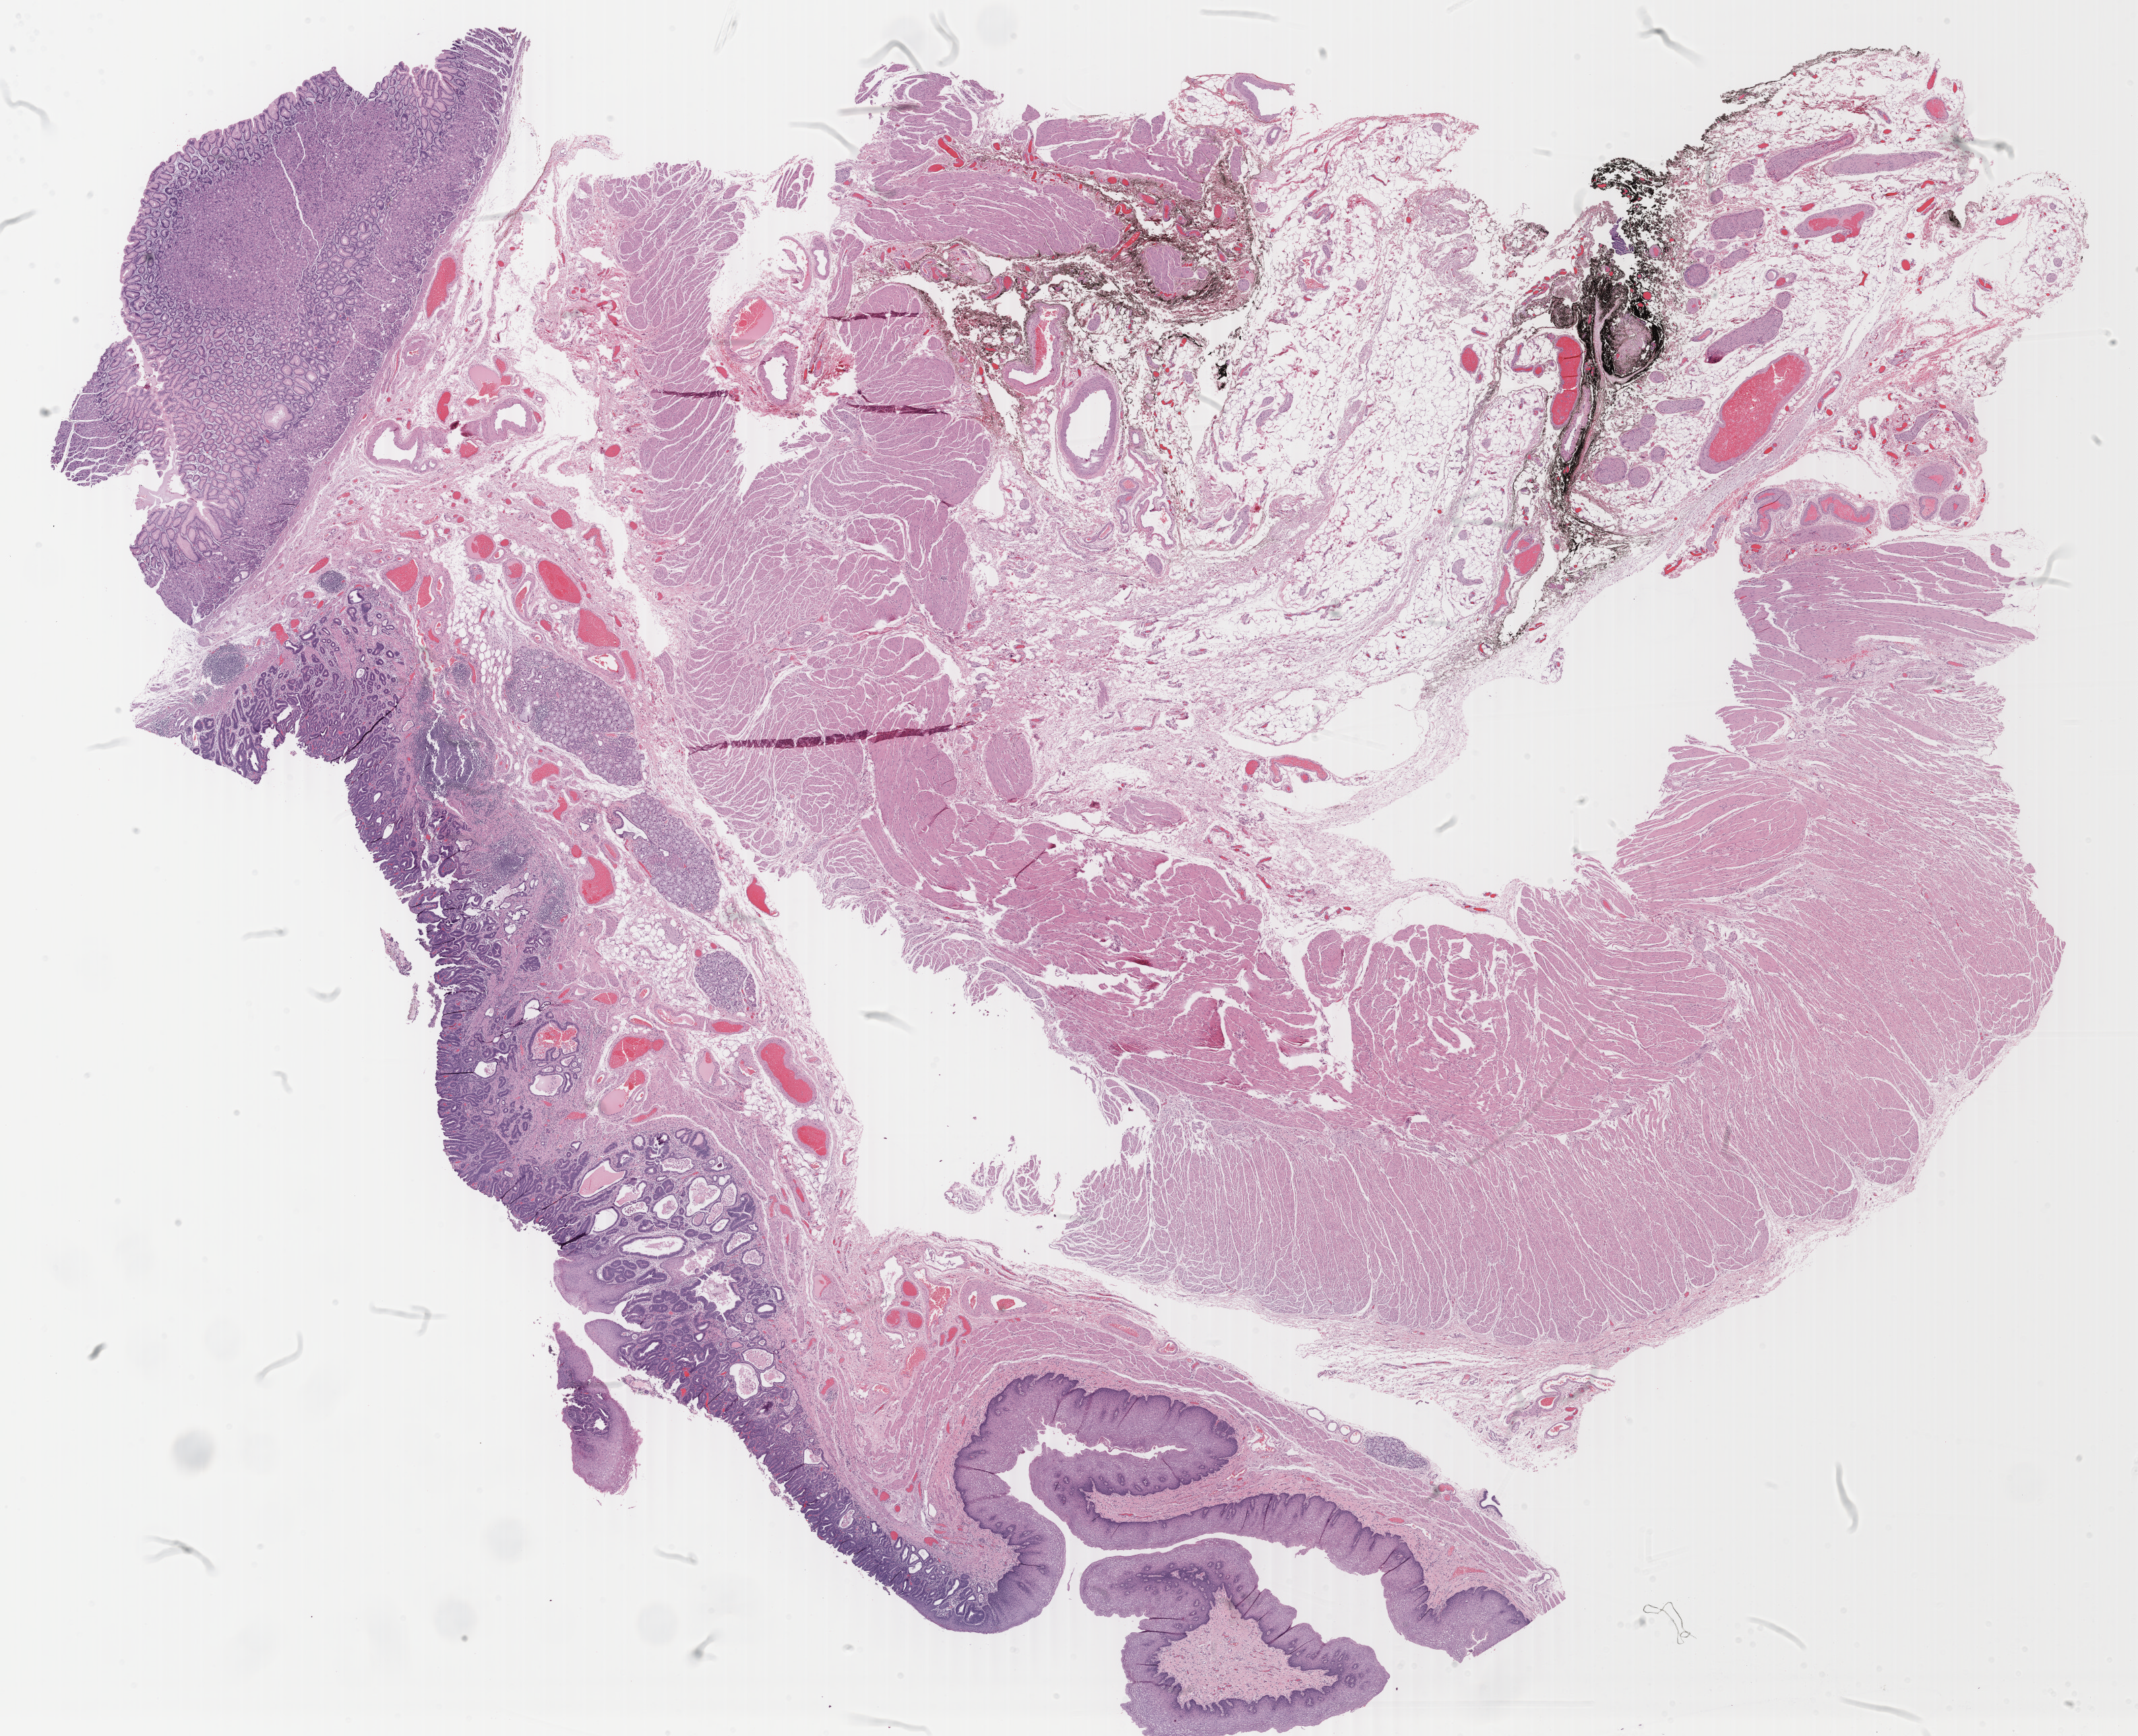
Whole-slide histology image, H&E-stained — a low-resolution overview of the entire scanned area, about 25.2 x 20.5 mm (from a 40x scan), formalin-fixed paraffin-embedded (FFPE) diagnostic section, primary tumour sample from the esophagus. Patient: female, age at initial diagnosis 79 years. Histologic grade: G1 (well differentiated).
- histologic diagnosis: Adenocarcinoma, NOS (lower third of esophagus)
- AJCC pathologic stage: I (7th edition)
- lymph nodes positive (case pathology): 0 of 5 examined